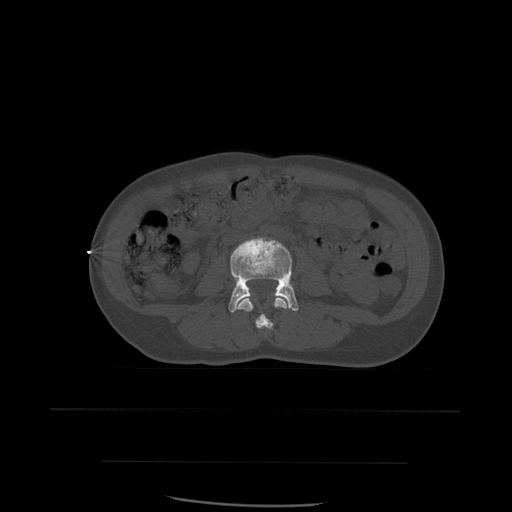
CT including the spine, one axial slice; position 181 of 574 along the scan axis; bone window (W 1800 / L 400 HU); 1.25 mm slice thickness; 512 × 512 image matrix, field of view 392 × 392 mm. Patient age 48 years. Case-level facts recorded for this patient, not image findings: primary cancer: lung; vertebrae with lytic lesions (as recorded): T11.
Structures marked on this image (semi-automatically segmented with operator editing):
- L3 vertebra: box from (x=235, y=297) to (x=287, y=331) px
- L4 vertebra: (x=229, y=237)–(x=299, y=313)